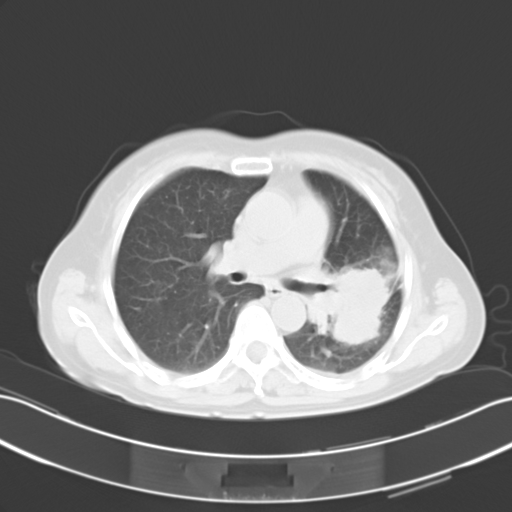
Chest CT, one axial slice; lung window (W 1500 / L -600 HU); 10 mm slice thickness; 512 × 512 image matrix, field of view 353 × 353 mm. Patient: female, 54 years. Case-level facts recorded for this patient, not image findings: clinical TNM (as recorded): T3 N1 M0.
Structures marked on this image (rectangle marked by the reading radiologist):
- lung tumour (recorded histology: adenocarcinoma): bounding box <307,259,388,348> (left, top, right, bottom; pixels)